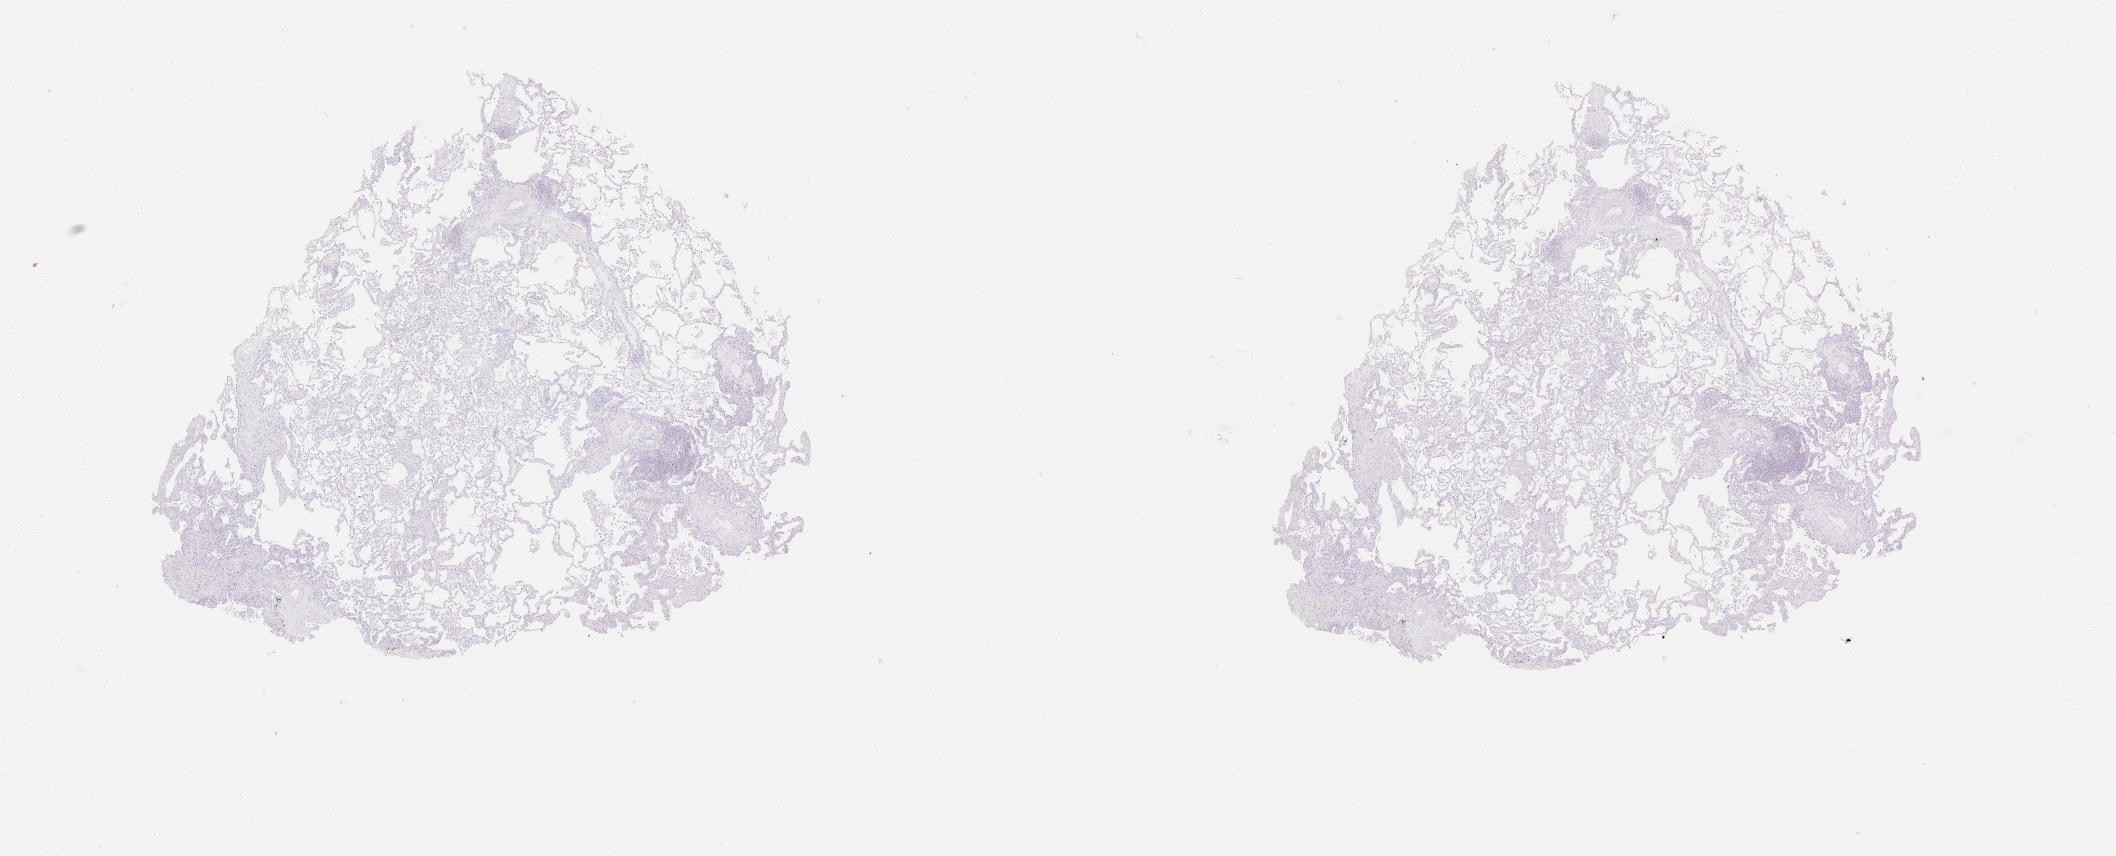
Whole-slide histology image, H&E-stained — low-resolution overview of the scanned area, about 17.0 x 6.9 mm. Normal (non-tumour) tissue sample, lung. 66-year-old male patient.
This section: normal (non-tumour) tissue from the same patient. Patient diagnosis (cohort enrolment): squamous cell carcinoma (lung).